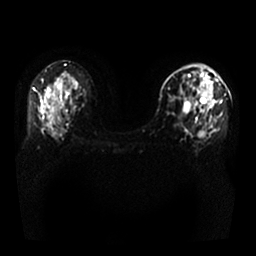
Breast MRI, one axial slice; position 15 of 25 along the scan axis; diffusion-weighted series; image 2 of 4 stored at this slice position (different b-values; order by instance number); 1.5 T; 256 × 256 image matrix. Female patient.
Annotated regions visible in this slice (outlined manually by an expert reader):
- tumour on diffusion-weighted imaging: box from (x=206, y=90) to (x=212, y=98) px